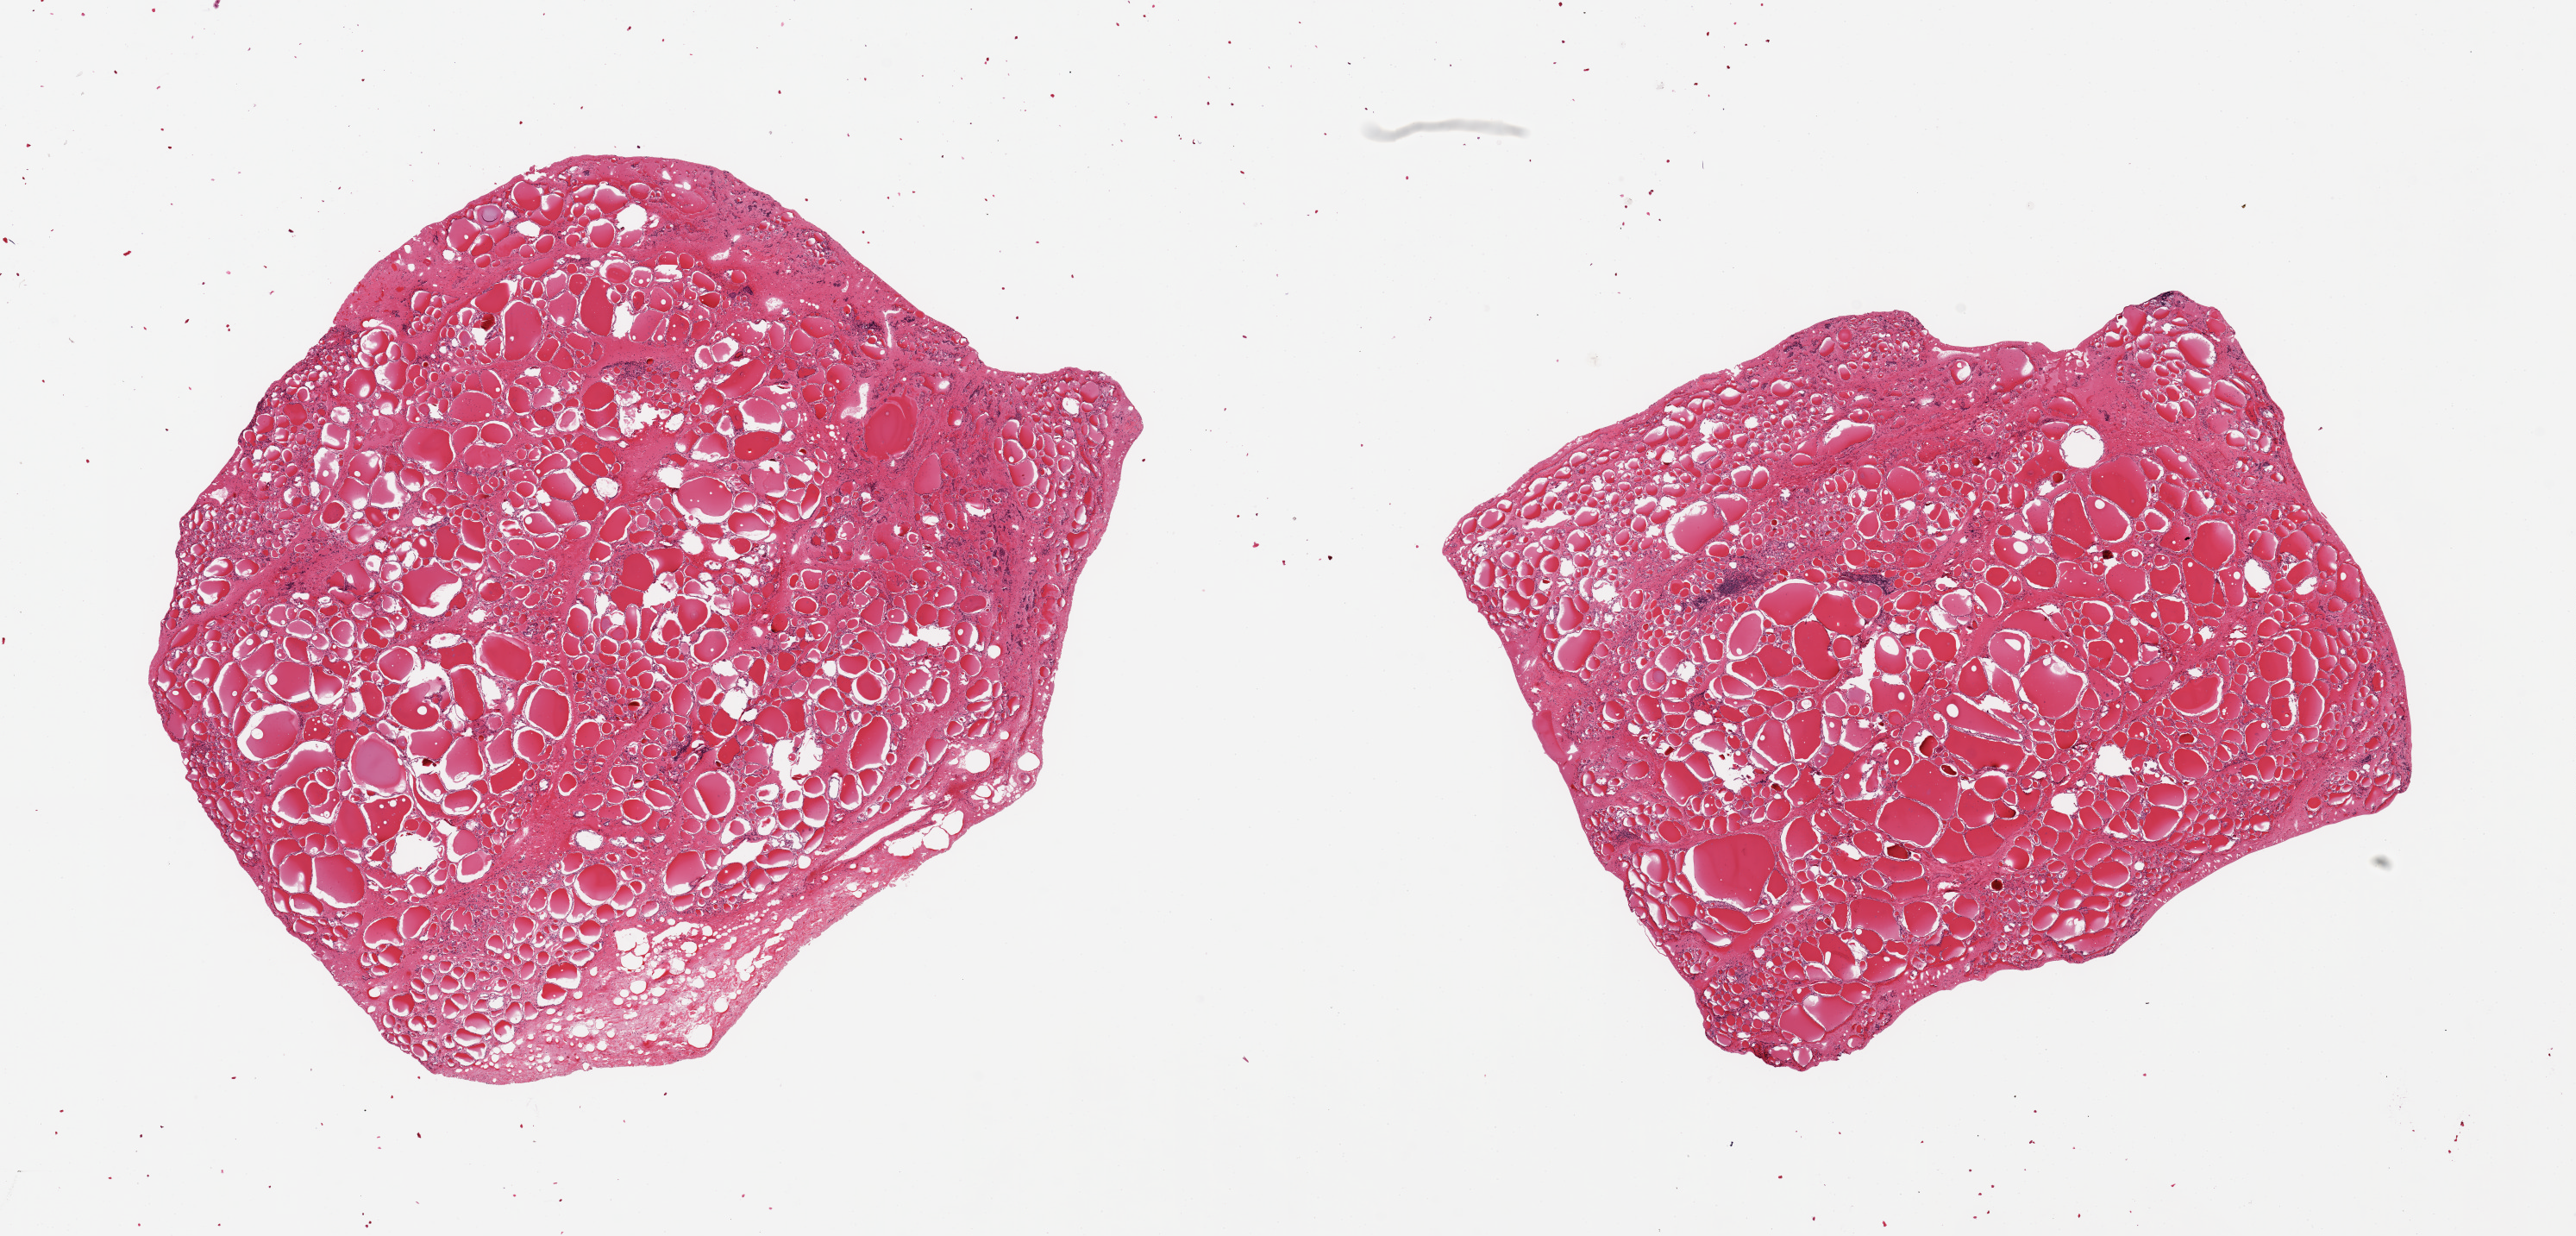
Whole-slide image, haematoxylin and eosin stain — low-resolution overview of the scanned area, about 23.6 x 11.3 mm (acquisition: 20x scan); PAXgene-fixed, paraffin-embedded tissue; target tissue: thyroid; donor tissue sample.
Reviewer comment on this tissue sample: 2 pieces 9x7 & 7x6 mm; small foci of lymphoid cells.